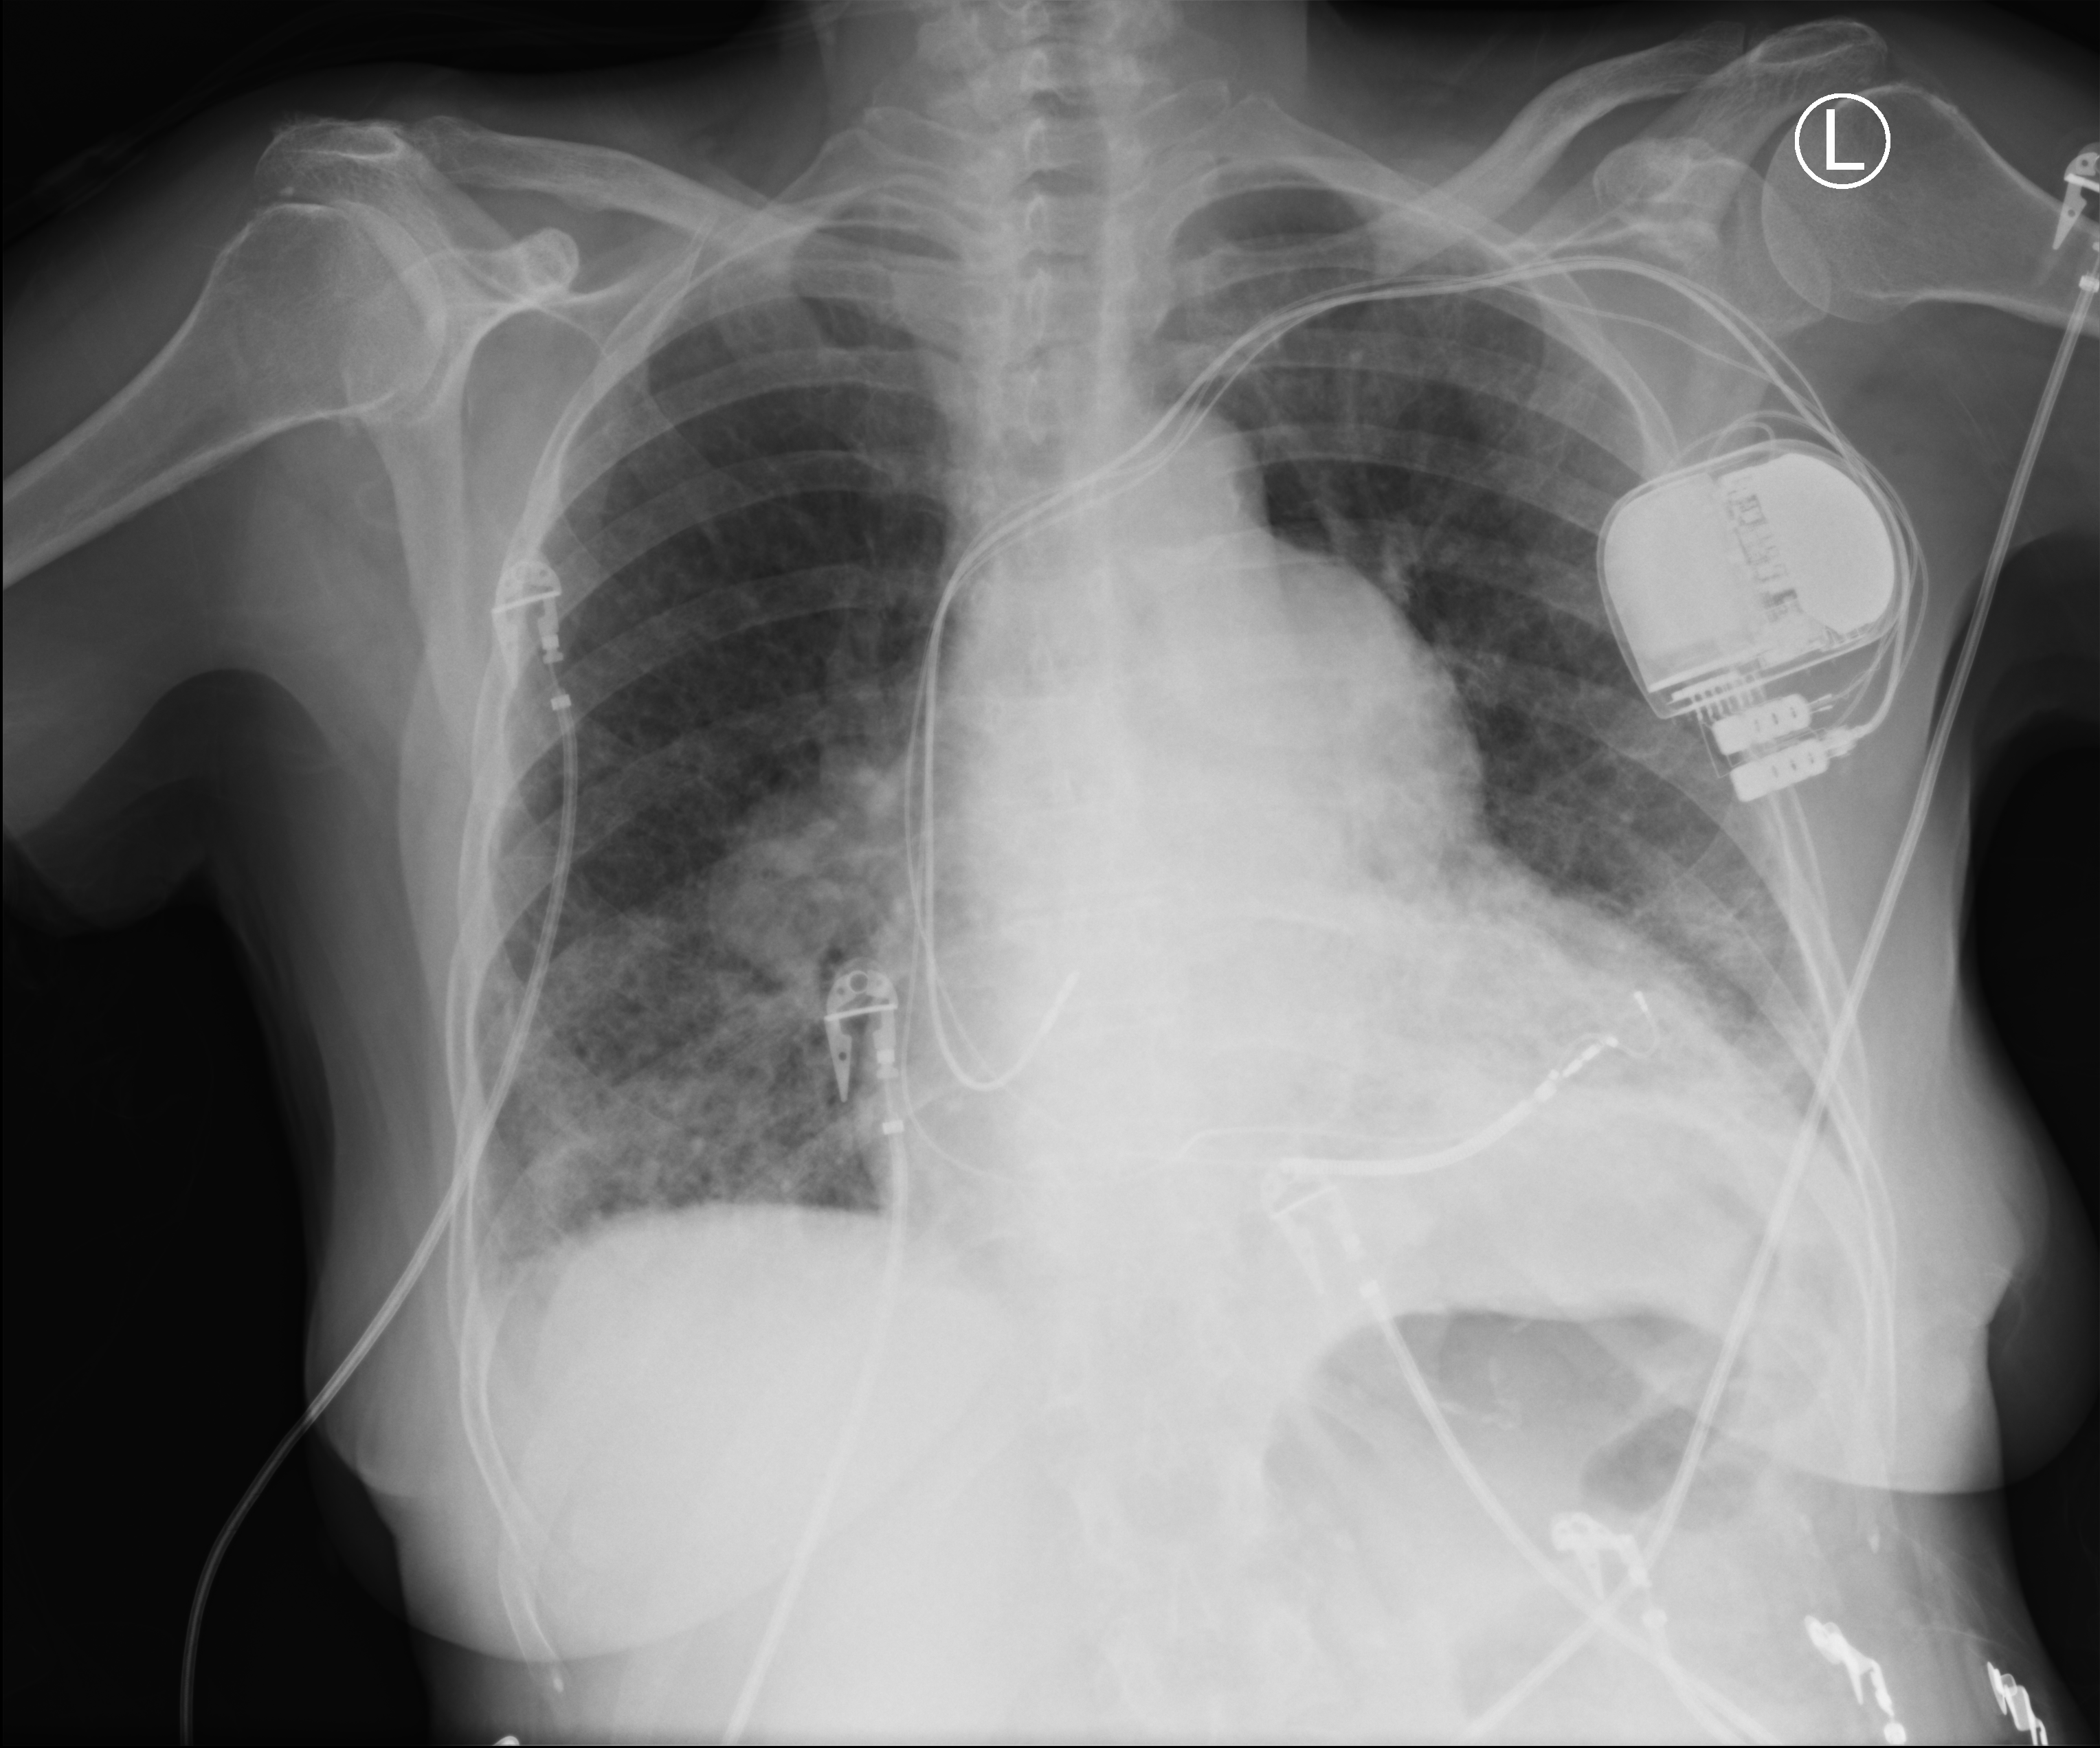
Chest X-ray (portable). Female patient hospitalised with COVID-19, age 60–74 years.
From the hospital-stay record, not from the radiograph (when in the stay this image was taken is not recorded): admitted to intensive care during this hospital stay: yes.